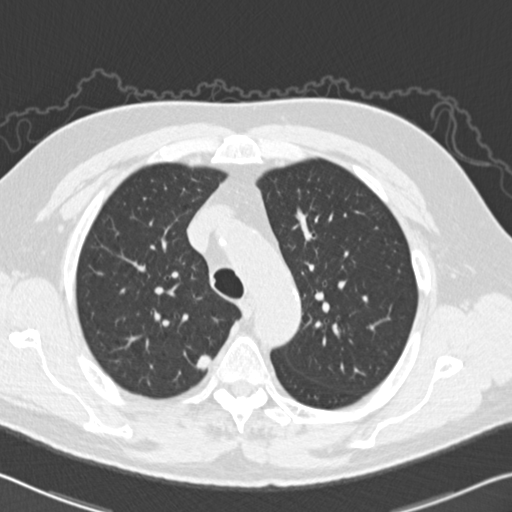
Low-dose screening chest CT, one axial slice. Slice 115 of 151 in the series (ordered by position). 120 kVp. Lung window (W 1500 / L -600 HU). 512 × 512 image matrix.
Annotated regions visible in this slice (manually delineated by an expert):
- lesion 1 (tumor, upper lobe of right lung): box from (x=196, y=355) to (x=212, y=370) px